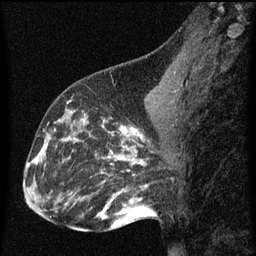
Breast MRI (dynamic contrast-enhanced), one sagittal slice. Slice 28 of 60 in the series (ordered by position). Dynamic contrast-enhanced series, image 2 of 3 at this slice position (ordered by acquisition). 1.5 T. TE 4.2 ms, TR 8 ms. 2 mm slice thickness. 256 × 256 image matrix, field of view 180 × 180 mm. Patient: female, 43 years.
Outlined on this slice (semi-automatic segmentation, software-assisted and operator-edited):
- analysis volume of interest (the breast-tissue region the enhancement analysis was run in; not a lesion): bounding box (x1, y1, x2, y2) in pixels: (53, 104, 101, 155)
- tumour enhancement mask (voxels above the 70 % enhancement threshold inside the analysis volume of interest): (55, 110, 90, 143)